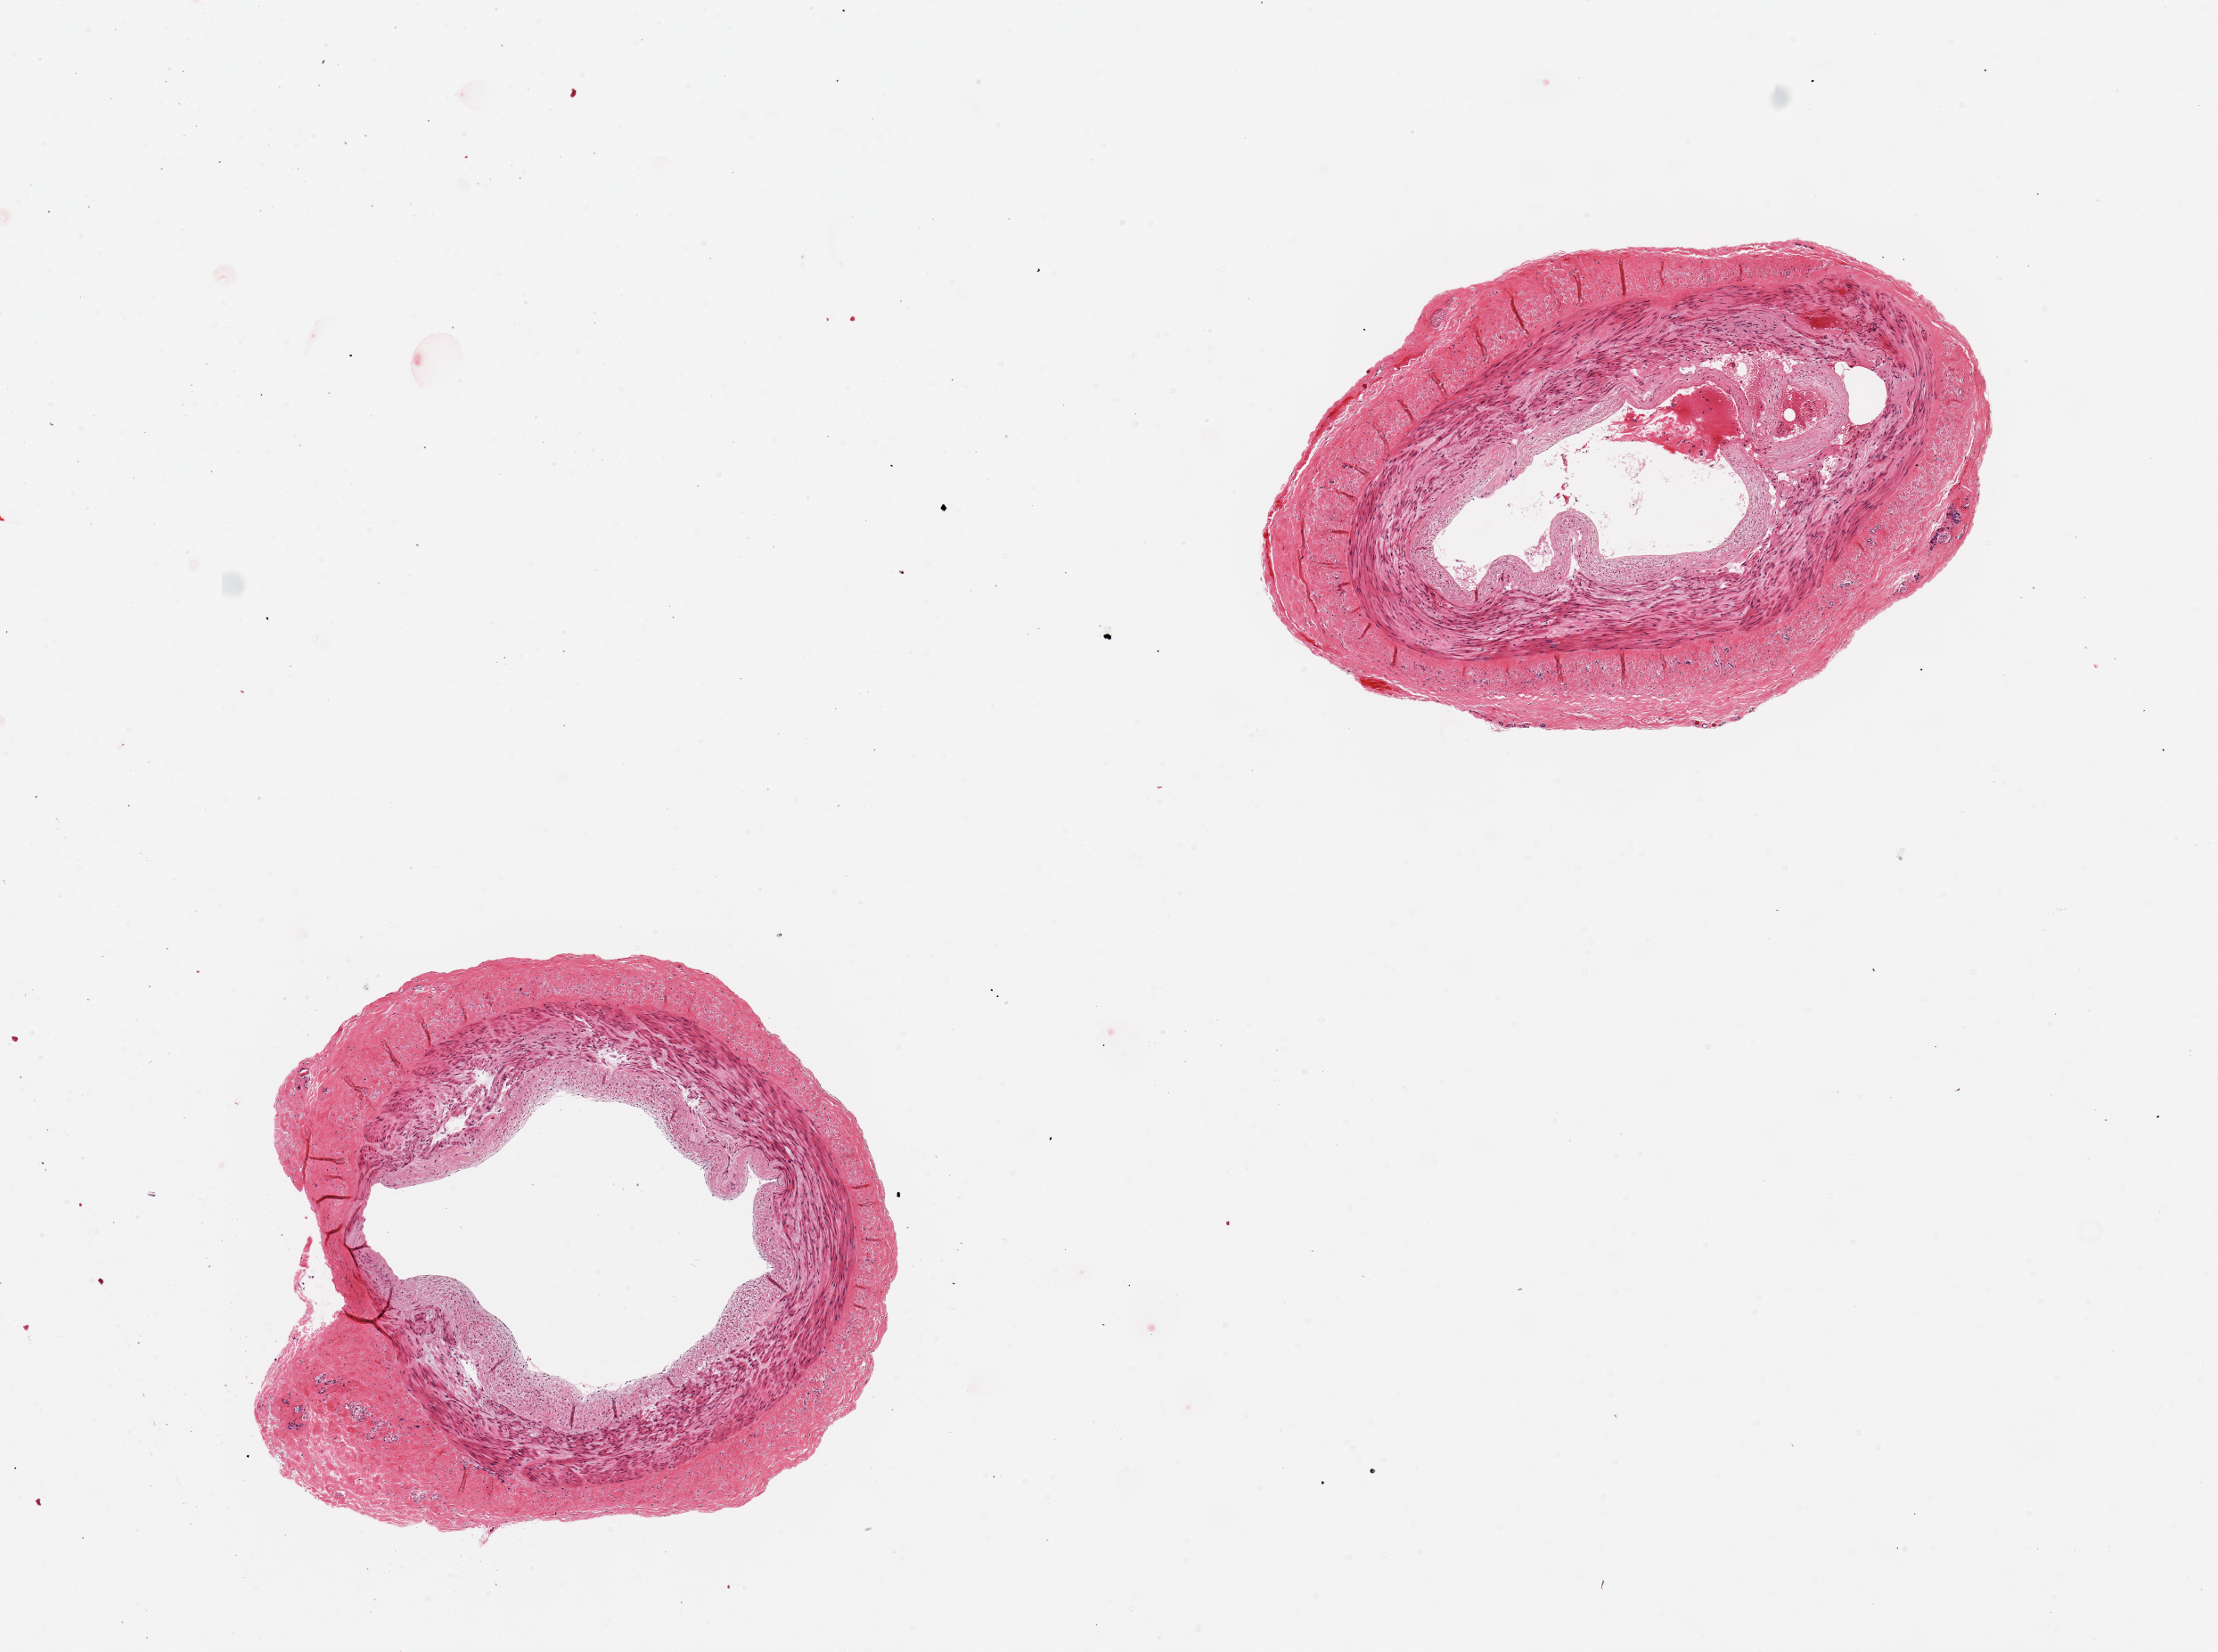
Digitized haematoxylin and eosin-stained section — low-resolution overview of the scanned area, about 9.8 x 7.3 mm. PAXgene-fixed paraffin-embedded (PFPE) section. Section of tibial artery (target tissue). Donor tissue sample.
Reviewer comment on this tissue sample: 2 pieces; some intimal thickening.